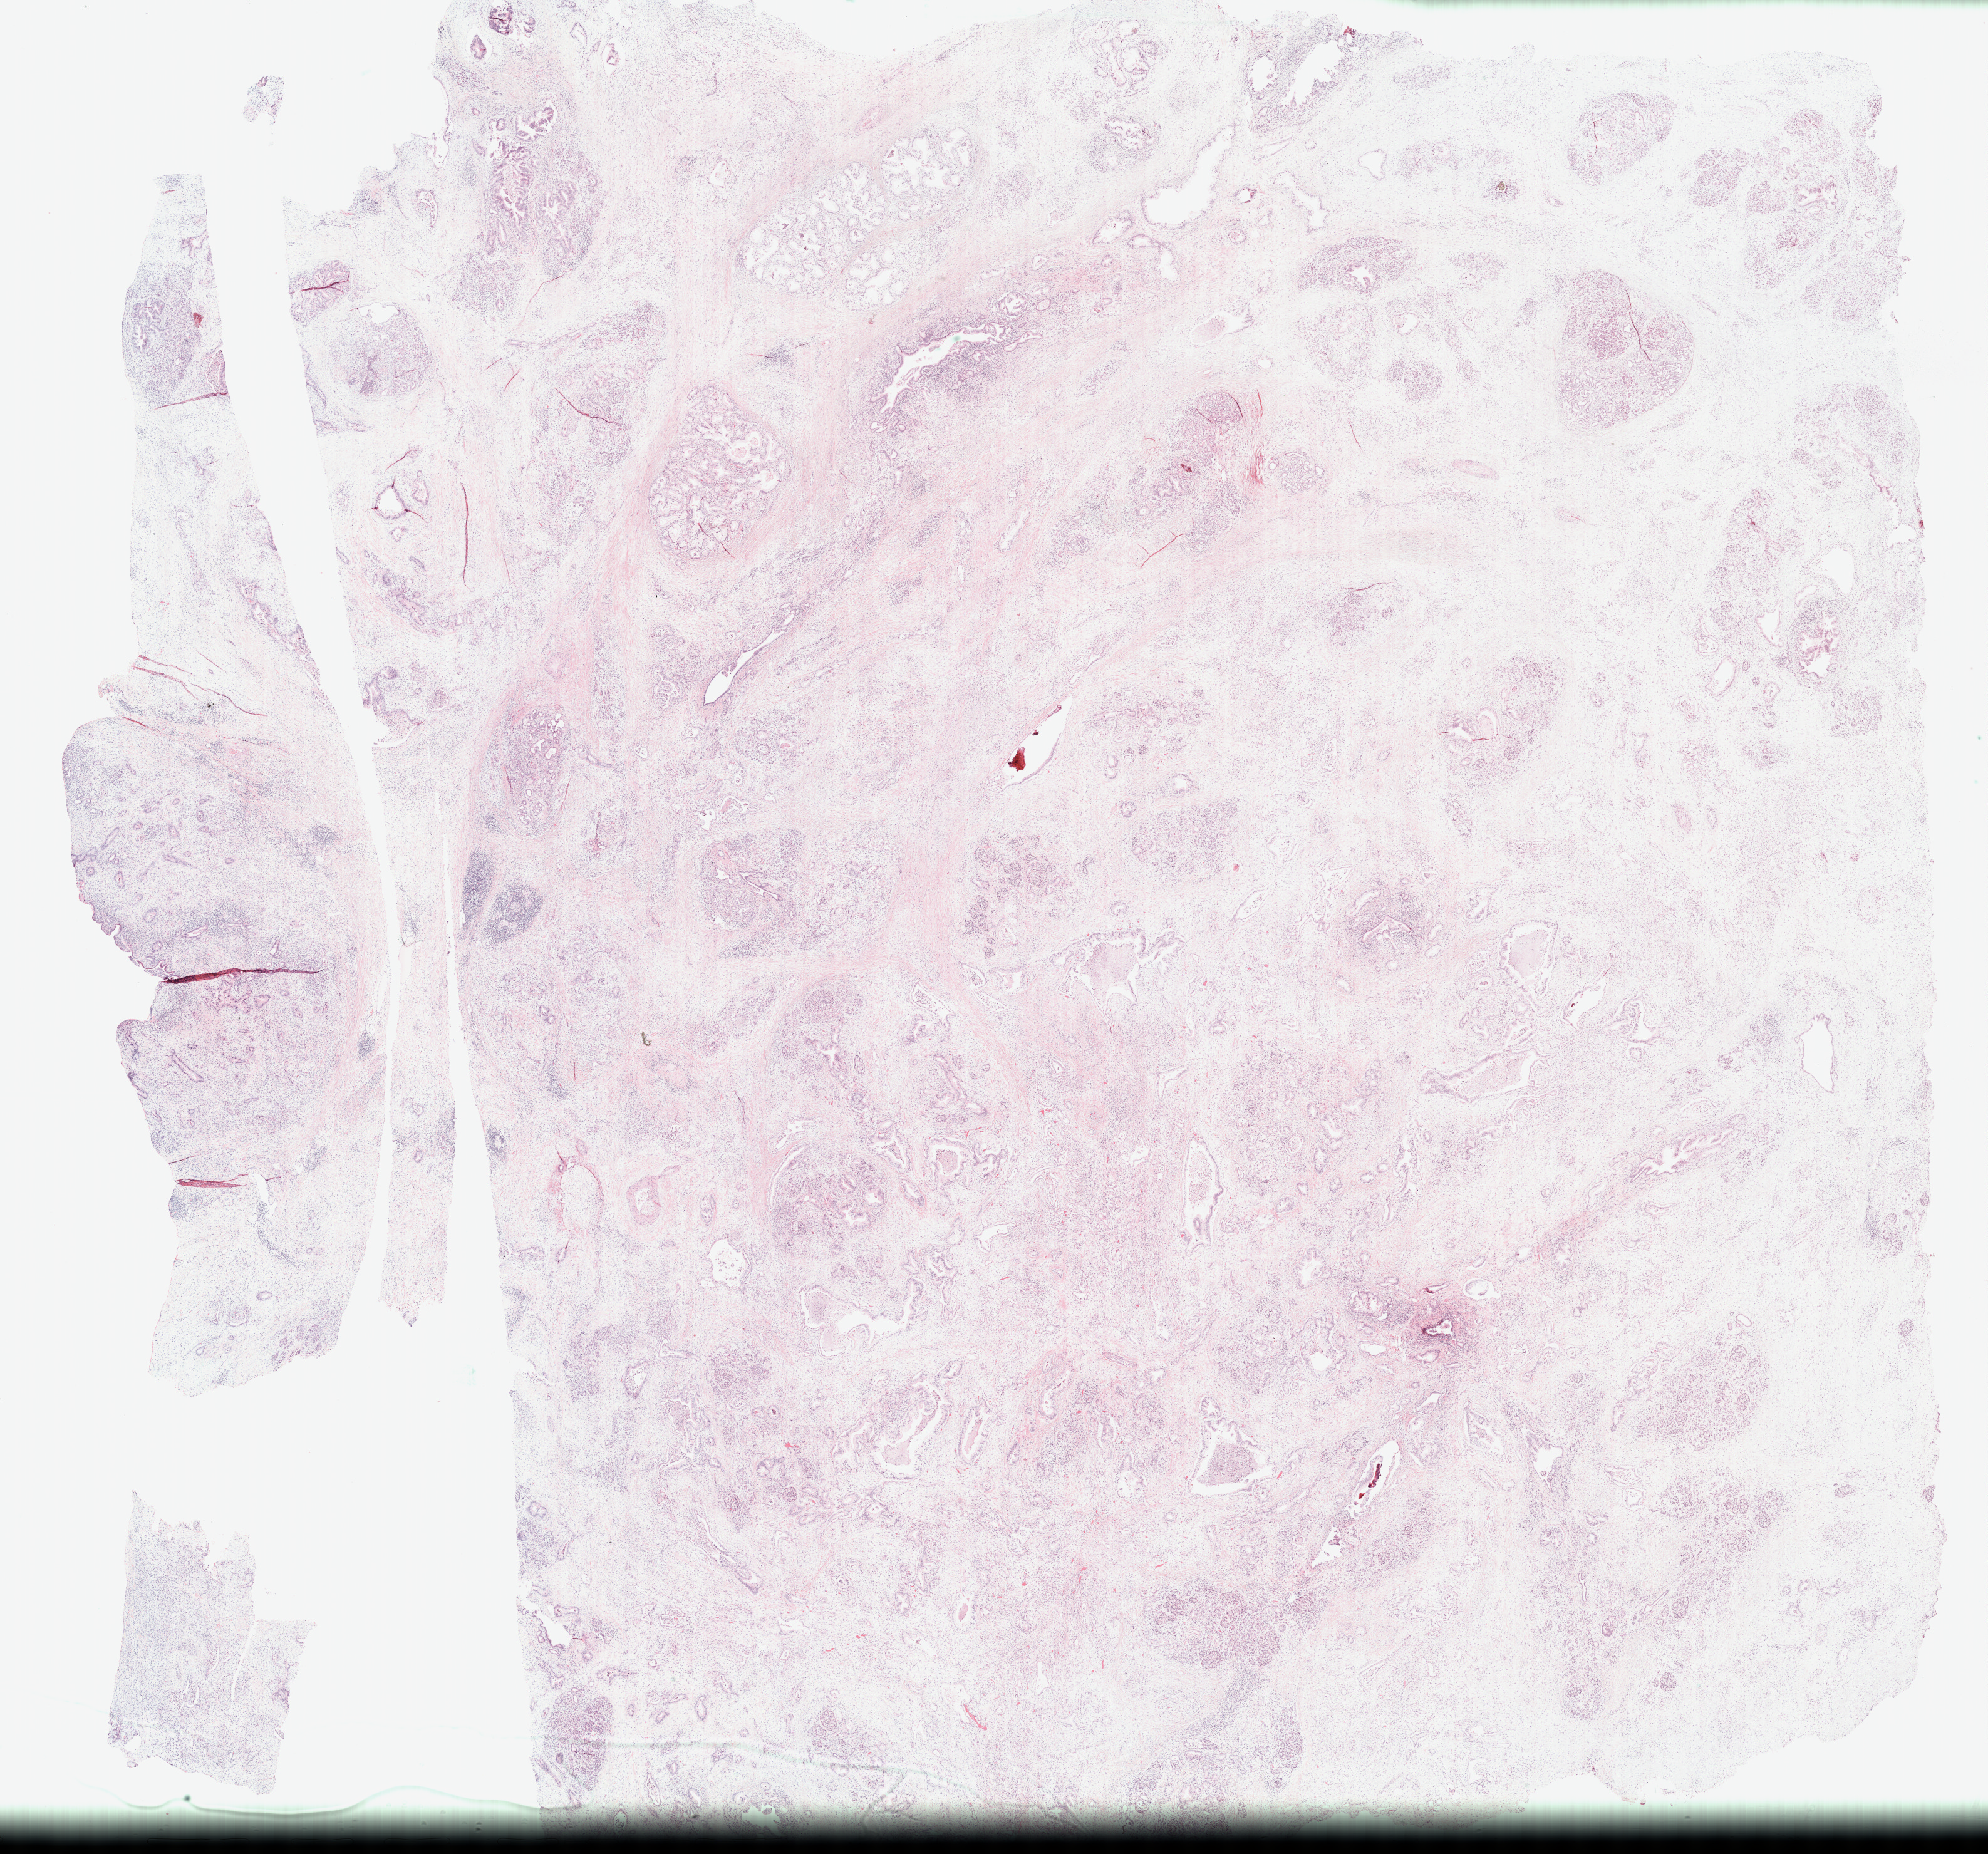
H&E-stained whole-slide image — shown as a low-resolution overview of the whole scanned area (about 25.7 x 23.9 mm, slide scanned at 40x), formalin-fixed paraffin-embedded (FFPE) diagnostic section, primary tumour sample from the pancreas. Female patient; age at initial diagnosis 44 years. Histologic grade: G1 (well differentiated).
Lymph nodes positive (case pathology): 5 of 17 examined. Histologic diagnosis: Infiltrating duct carcinoma, NOS (head of pancreas). AJCC pathologic stage: IIB.